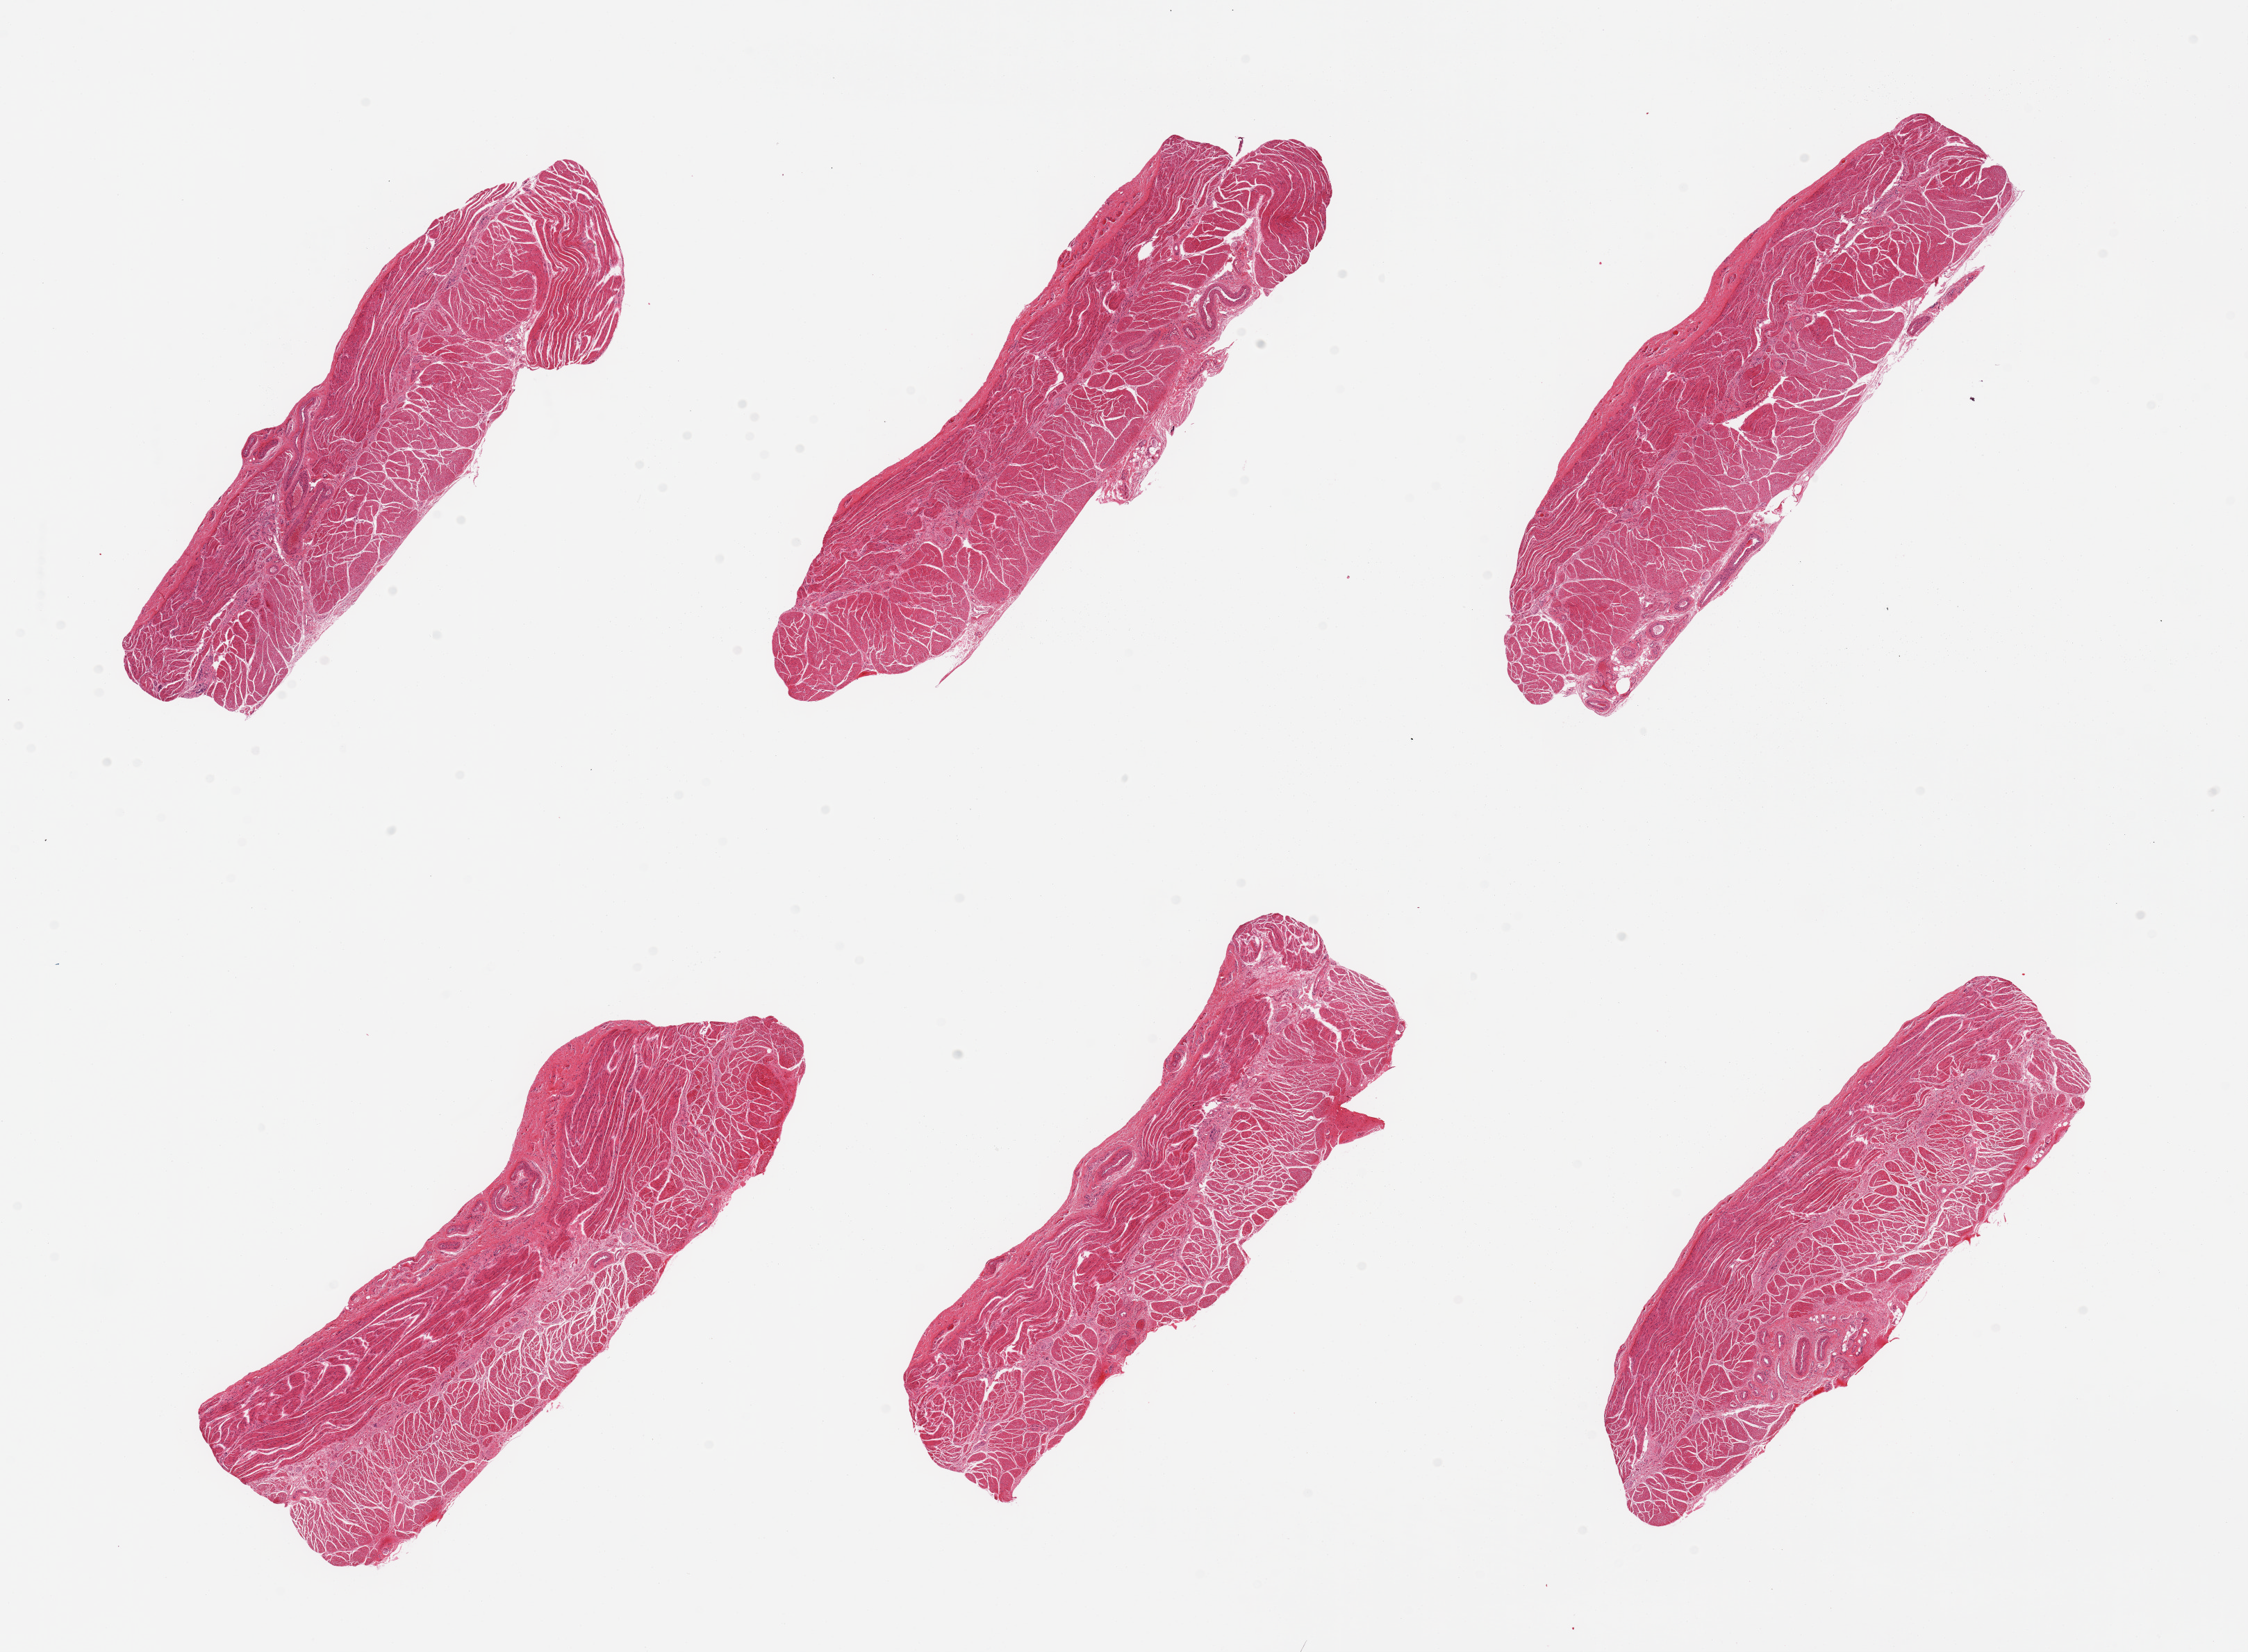
Digitized haematoxylin and eosin-stained section — shown as a low-resolution overview of the whole scanned area (about 25.6 x 18.8 mm, from a 20x scan). PAXgene-fixed paraffin-embedded (PFPE) section. Section of esophageal muscle (target tissue). Donor tissue sample. Female donor.
Reviewer comment on this tissue sample: 6 pieces, all muscularis, good specimens.